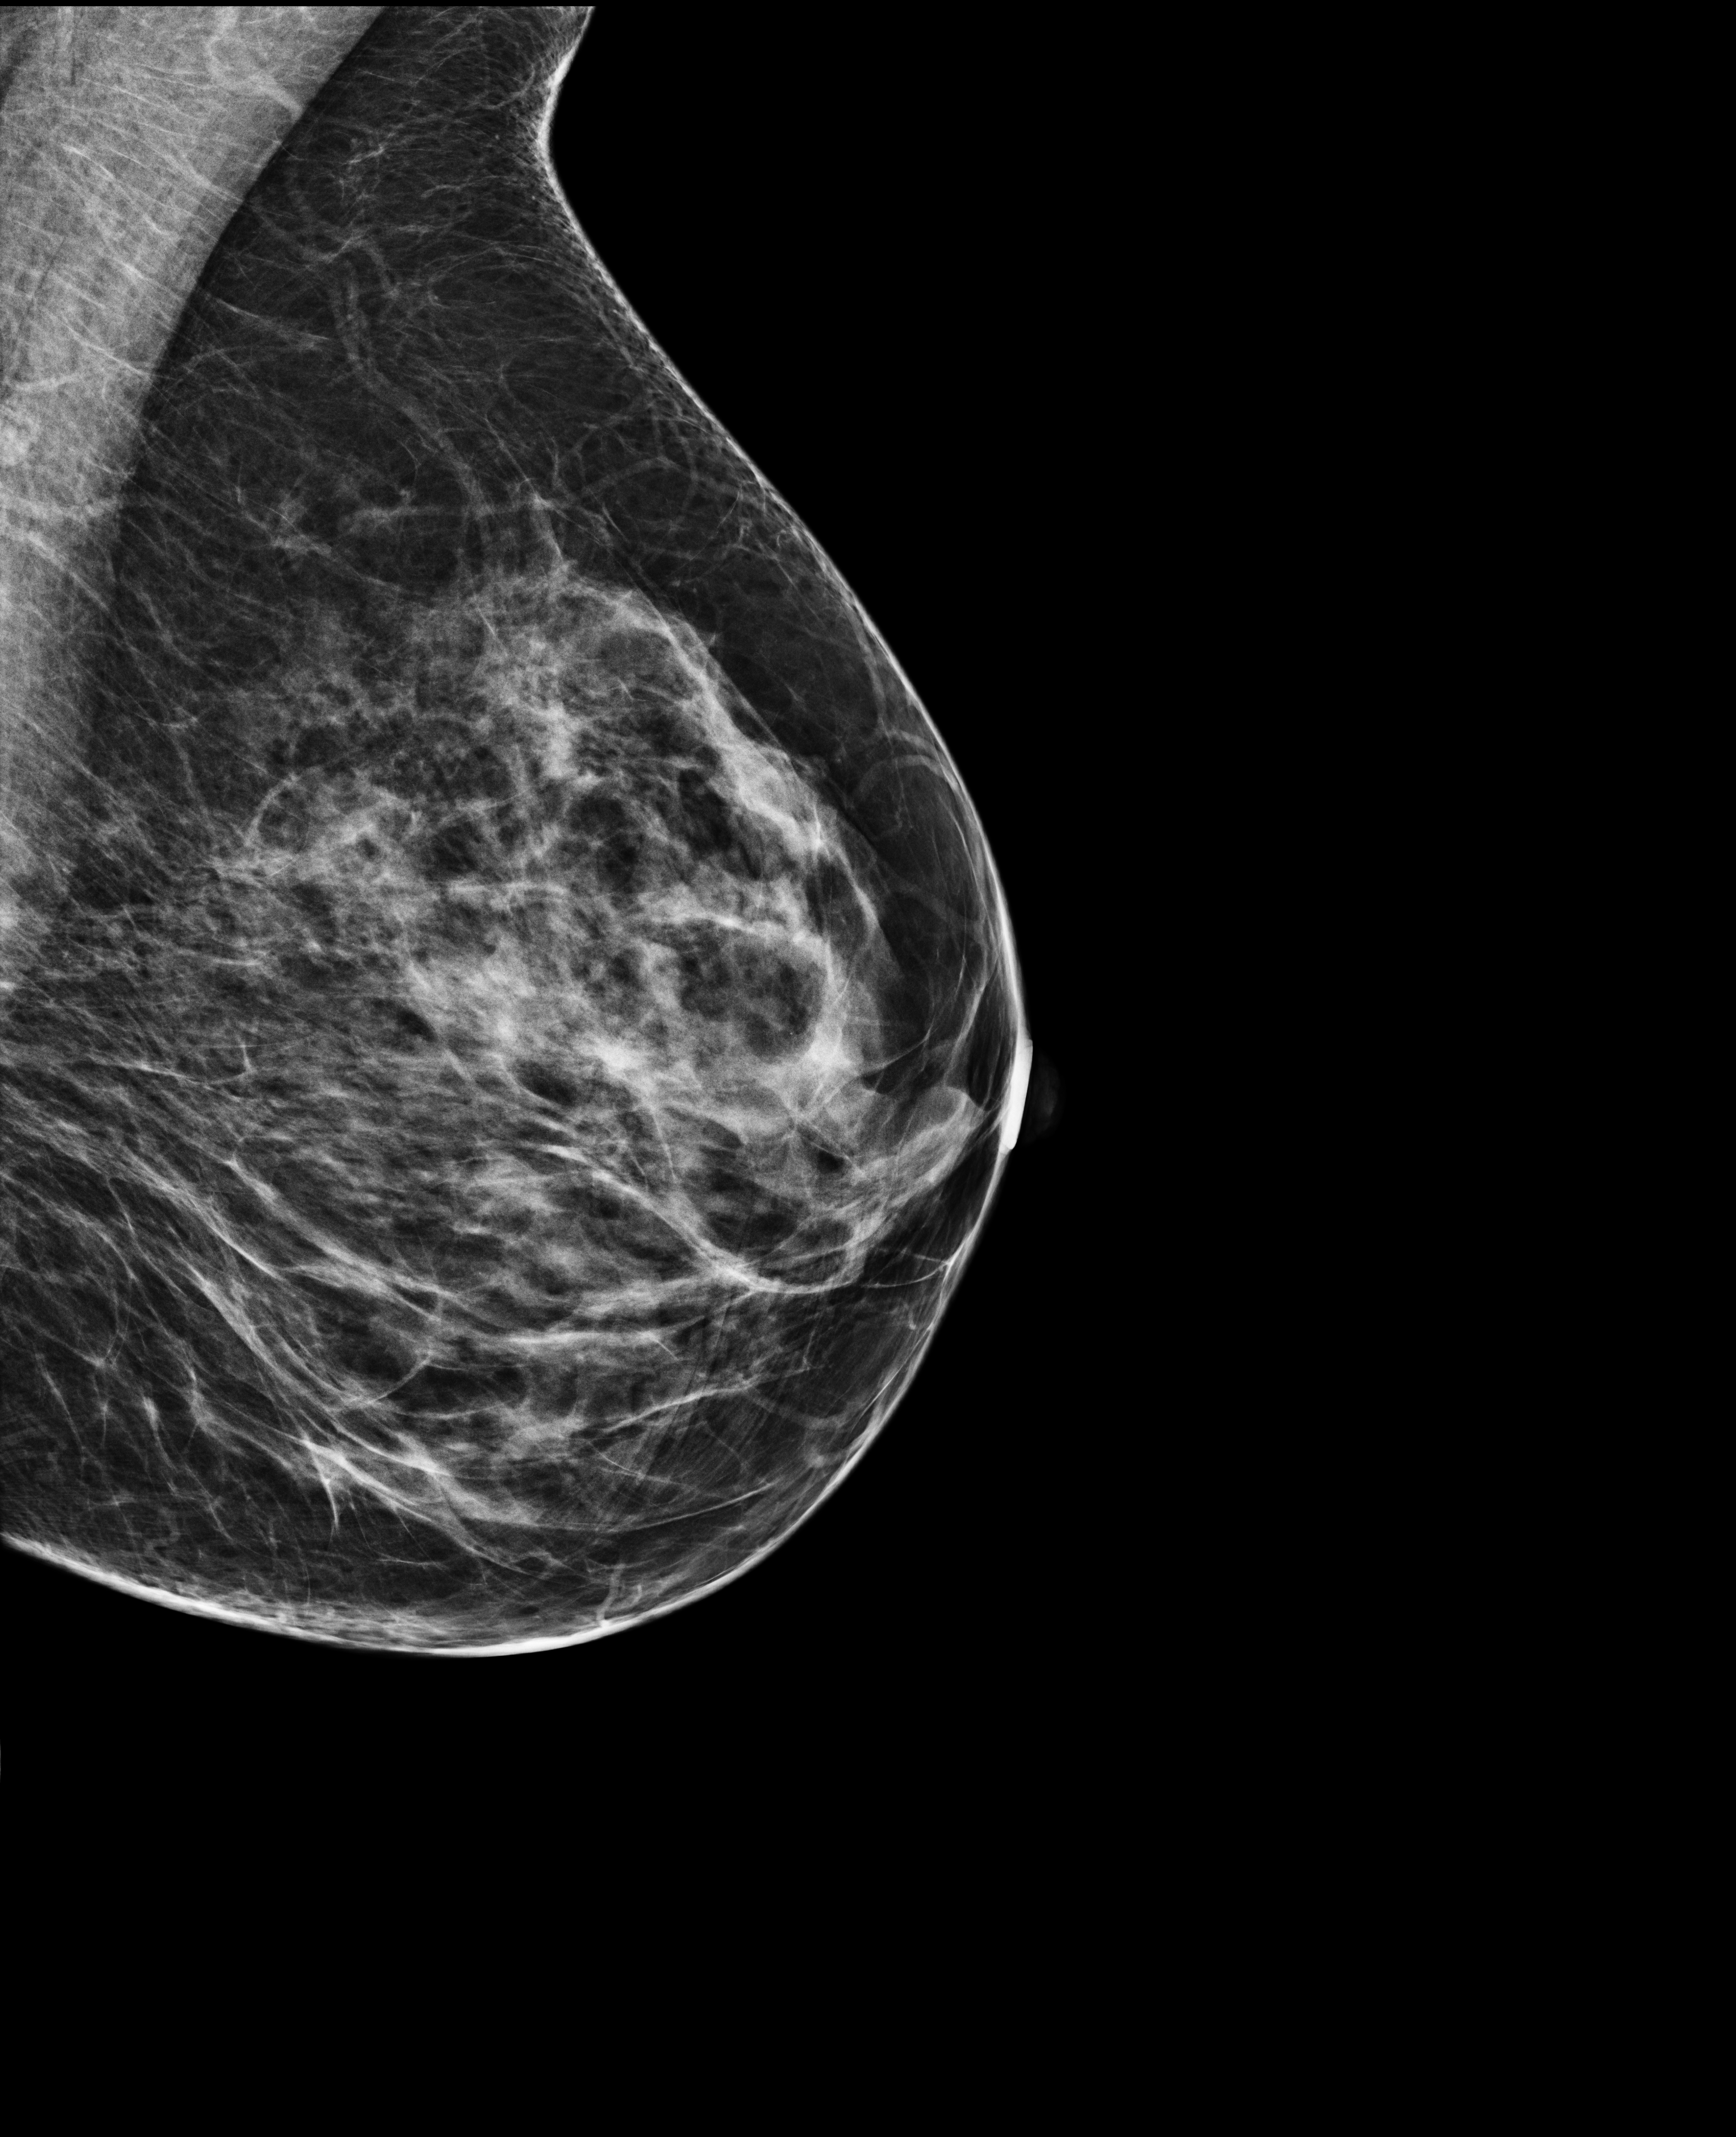
Full-field digital mammogram (FFDM), left breast, medio-lateral oblique projection, annual screening mammography examination, compressed breast thickness 56 mm, system: Selenia Dimensions. Female patient, age 53 years.
Breast density at the screening exam (both breasts): scattered fibroglandular densities (BI-RADS density category b). Final BI-RADS assessment for this screening round (tomosynthesis exam, both breasts): category 1. Recall: no recall after this screen.